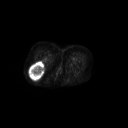
FDG PET of an extremity soft-tissue mass (from a PET/CT study), one axial slice. Slice 39 of 267 in the series (ordered by position). 3.27 mm slice thickness. 128 × 128 image matrix, field of view 700 × 700 mm. Female patient, age 70 years. Case-level facts recorded for this patient, not image findings: histological type: synovial sarcoma; grade: intermediate; site of the primary tumour: right buttock.
Annotated regions visible in this slice (expert contour drawn on MRI and transferred to this co-registered scan by the dataset authors):
- gross tumour volume including surrounding oedema: bounding box [x1, y1, x2, y2] px = [29, 61, 44, 79]
- gross tumour volume (mass): [29, 62, 44, 79]